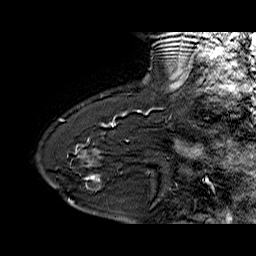
Breast MRI (dynamic contrast-enhanced), one sagittal slice; slice 47 of 60 in the series (ordered by position); dynamic contrast-enhanced series, time point 2 of 6 at this slice position (early post-contrast); 1.5 T; TE 6.4 ms, TR 32.9 ms; 256 × 256 image matrix, field of view 200 × 200 mm. Female patient. Case-level facts recorded for this patient, not image findings: setting: breast cancer imaged before/during neoadjuvant chemotherapy; receptor status: HR-positive, HER2-negative.
Outlined on this slice (semi-automatically segmented with operator editing):
- analysis volume of interest (the breast-tissue region the enhancement analysis was run in; not a lesion): bounding box [x1, y1, x2, y2] px = [68, 154, 126, 203]
- tumour enhancement mask (voxels above the 100 % enhancement threshold inside the analysis volume of interest): [87, 175, 99, 182]